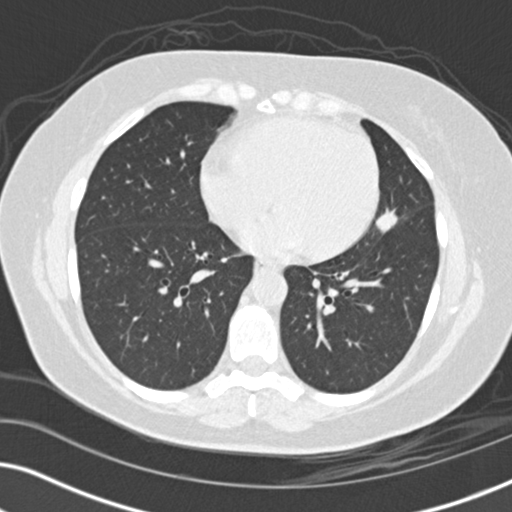
Low-dose screening chest CT, one axial slice. Position 67 of 152 along the scan axis. Reconstruction kernel B30f. 120 kVp. Lung window (W 1500 / L -600 HU). 2 mm slice thickness. 512 × 512 image matrix.
Structures marked on this image (outlined manually by an expert reader):
- lesion 1 (tumor, upper lobe of left lung): bounding box <376,211,398,232> (left, top, right, bottom; pixels)